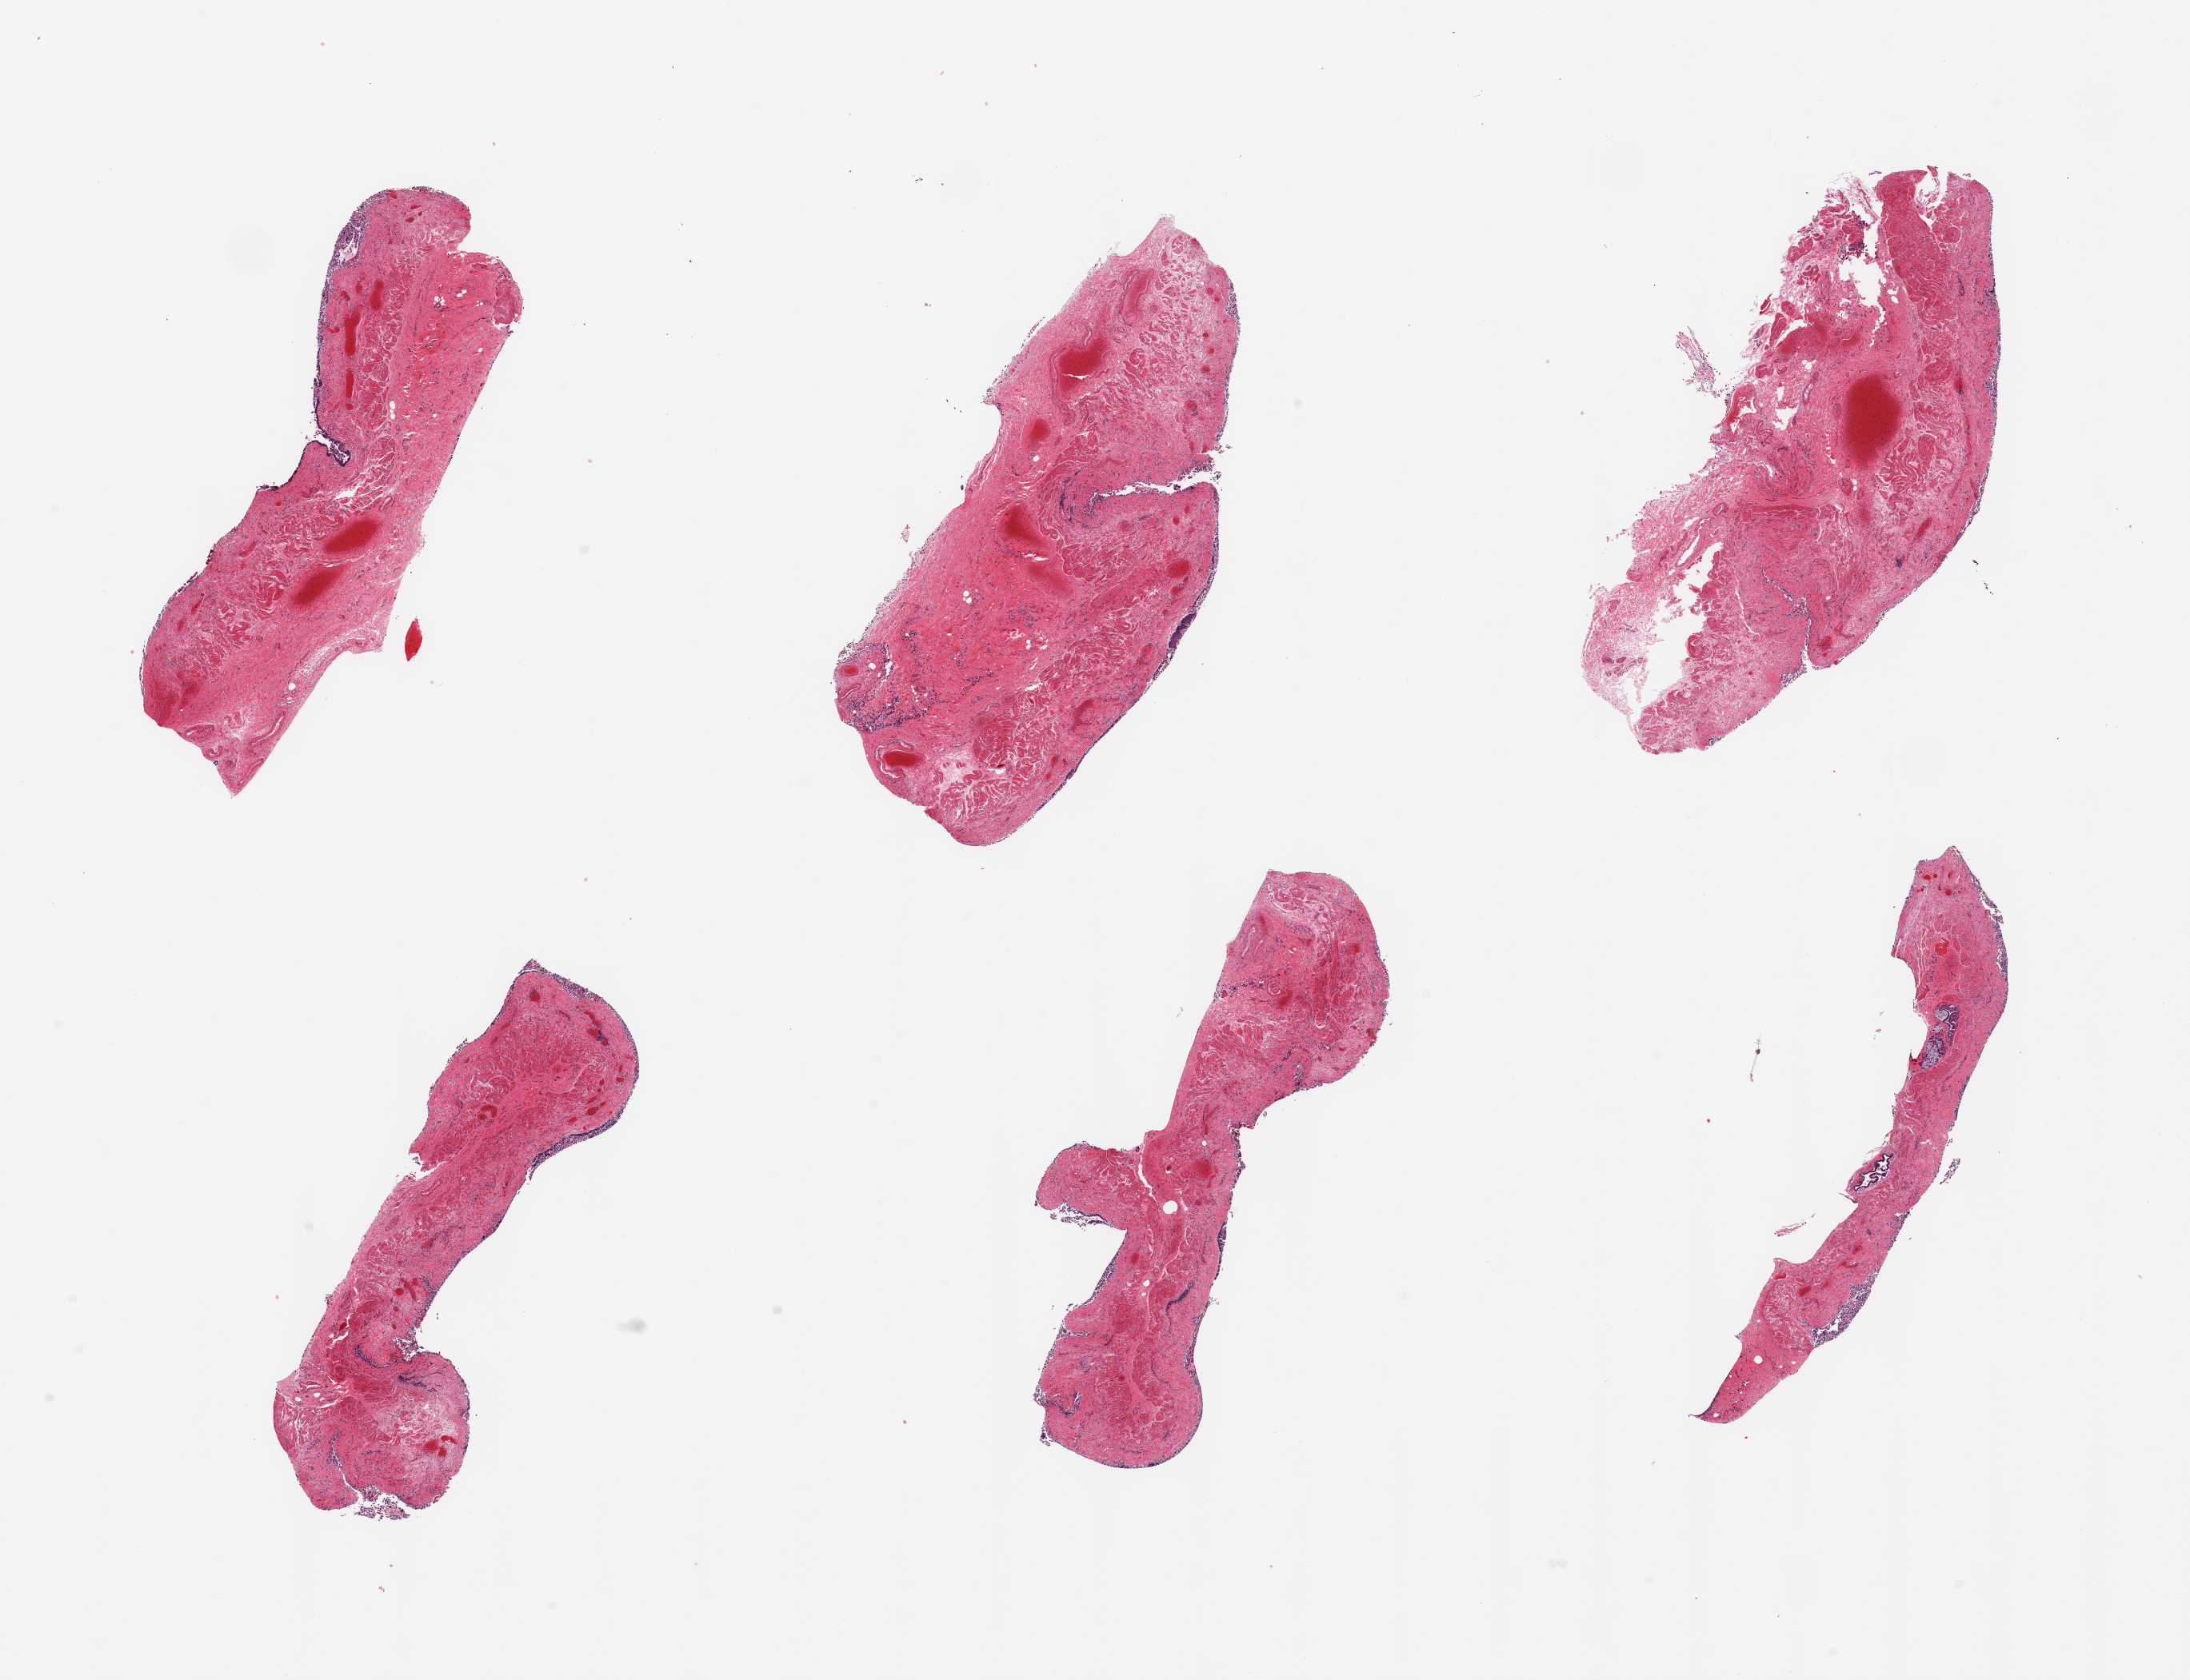
Digitized haematoxylin and eosin-stained section, low-resolution overview of the scanned area, about 21.7 x 16.6 mm; PAXgene-fixed, paraffin-embedded tissue; section of esophageal mucous membrane (target tissue); tissue donor sample. Male donor.
Pathologist's review note for this sample: 6 pieces, squamous mucosa badly autolyzed, largelky sloughed. Unusually poorly preserved.